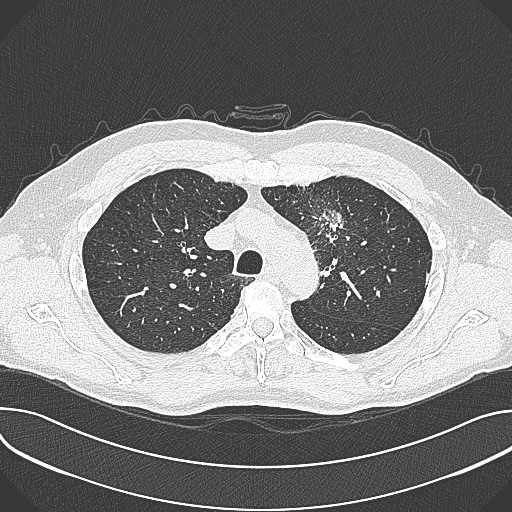
Chest CT (low-dose screening protocol), one axial image, baseline annual screen, lung window (W 1500 / L -600 HU), 120 kVp, slice 89 of 361 in the series. Male, age 59 years at enrolment.
Expert-annotated lung lesion, bounding box (x1, y1, x2, y2) in pixels: (301, 200, 358, 258). The screening reader recorded 2 non-calcified nodules or masses ≥4 mm on this exam (left upper lobe, left upper lobe); which of them this box marks is not recorded. Official screen result: positive, change unspecified: nodule(s) >= 4 mm or enlarging nodule(s), mass(es), or other non-specific abnormalities suspicious for lung cancer. Lung cancer was diagnosed 21 days after this screen: non-small cell carcinoma, left upper lobe, poorly differentiated (G3), stage IIIA (AJCC 6th edition), 35 mm at pathology.